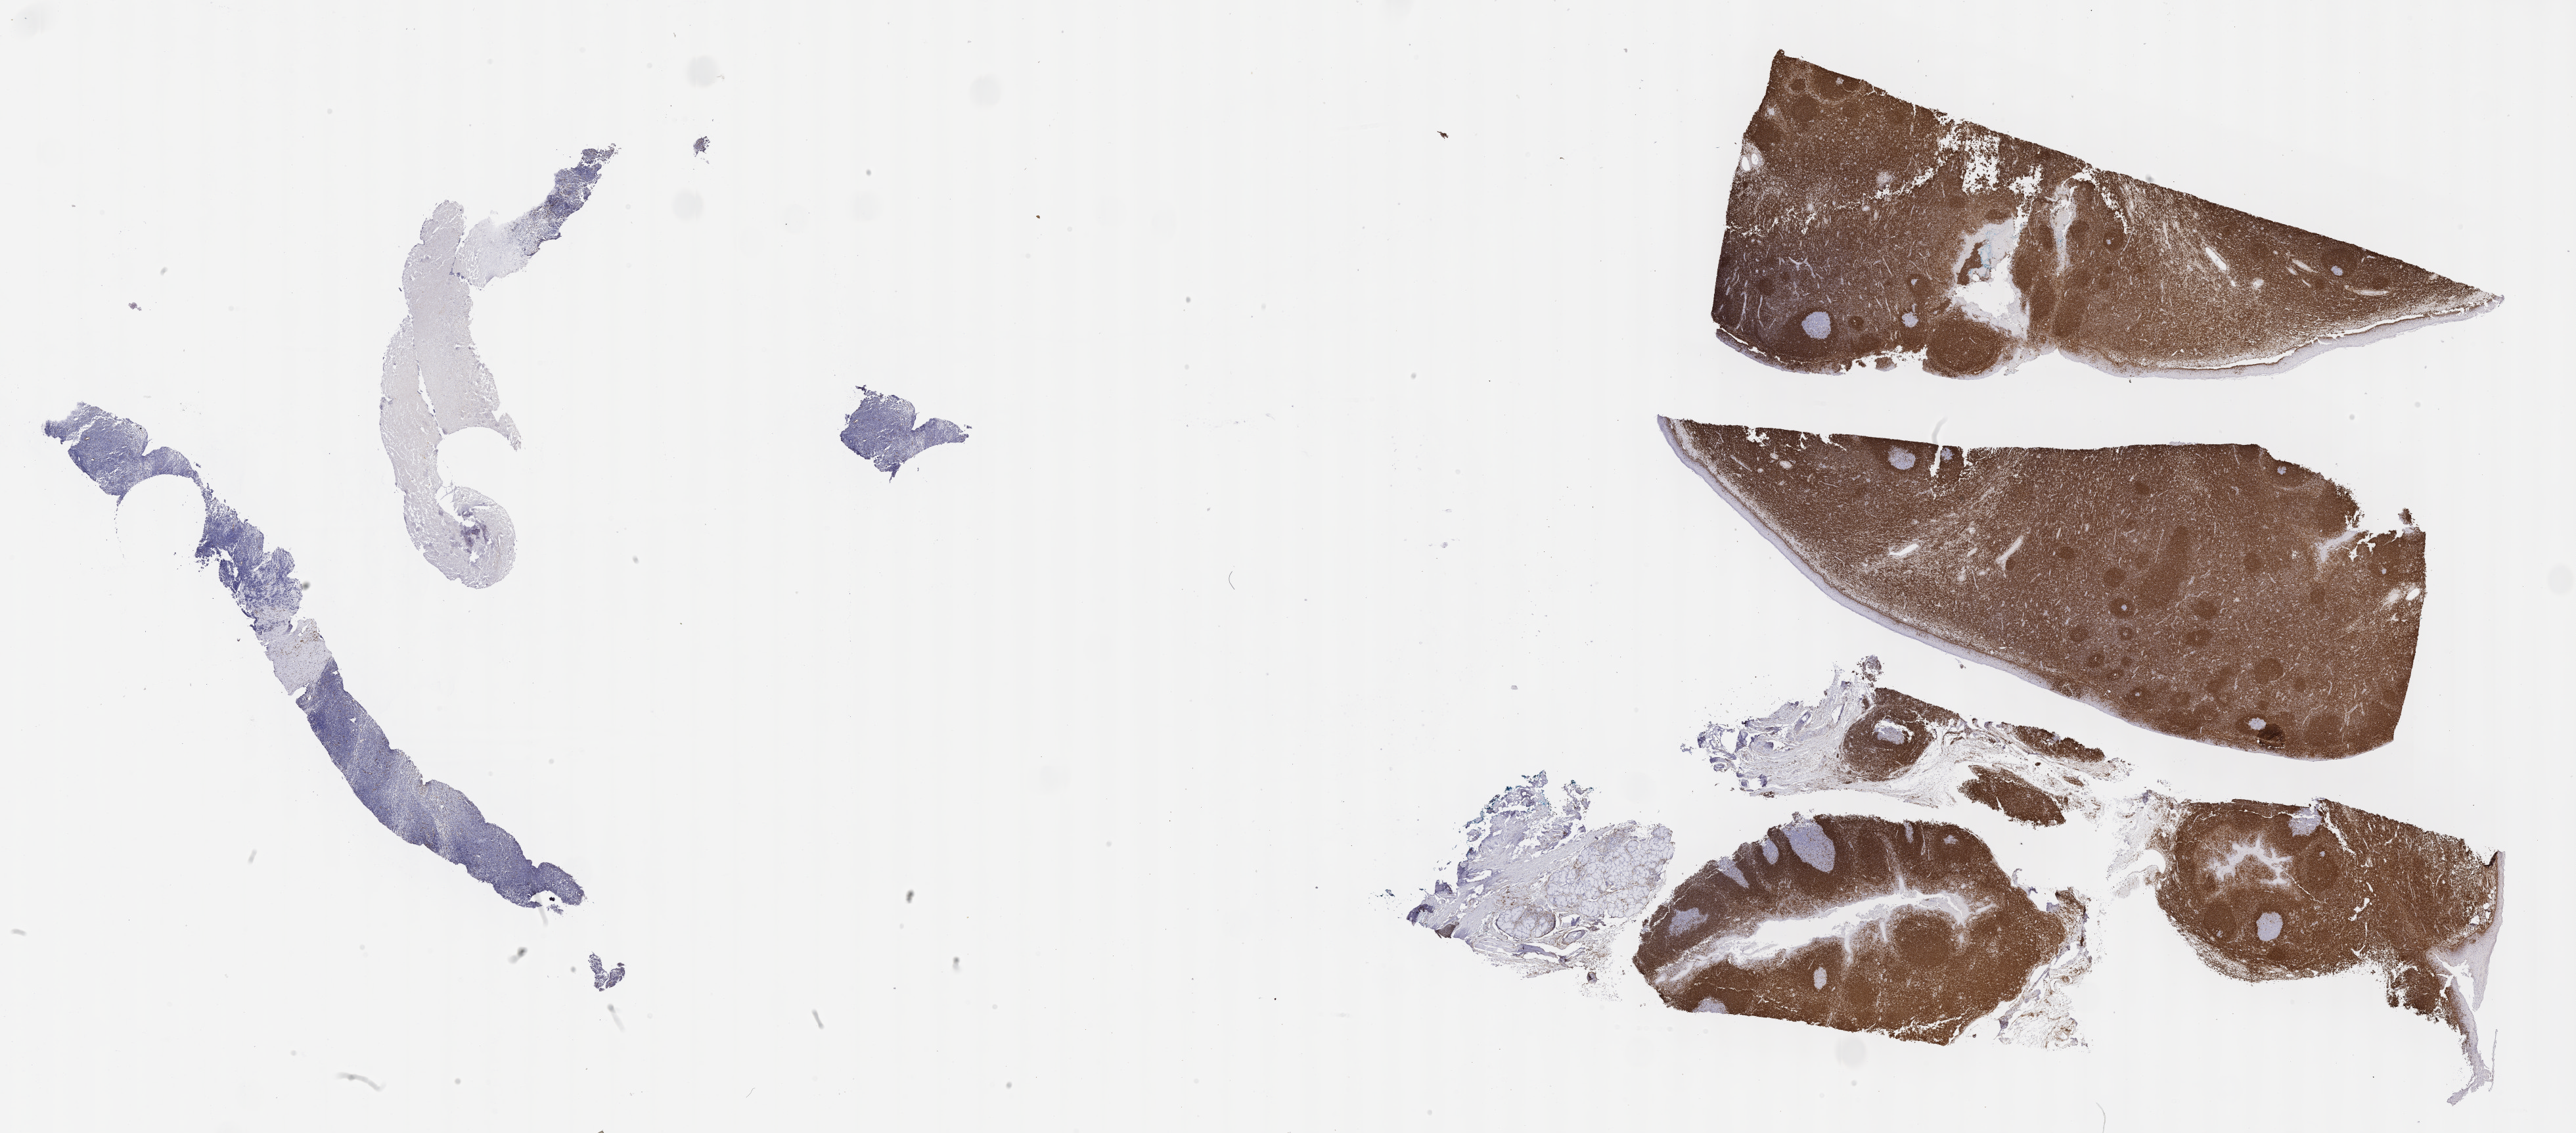
Immunohistochemistry (IHC) whole-slide image stained for BCL2 — low-resolution overview of the scanned area, about 31.7 x 13.9 mm, specimen: tumor tissue. Patient: male, aged 10.
• diagnosis: Burkitt lymphoma, NOS